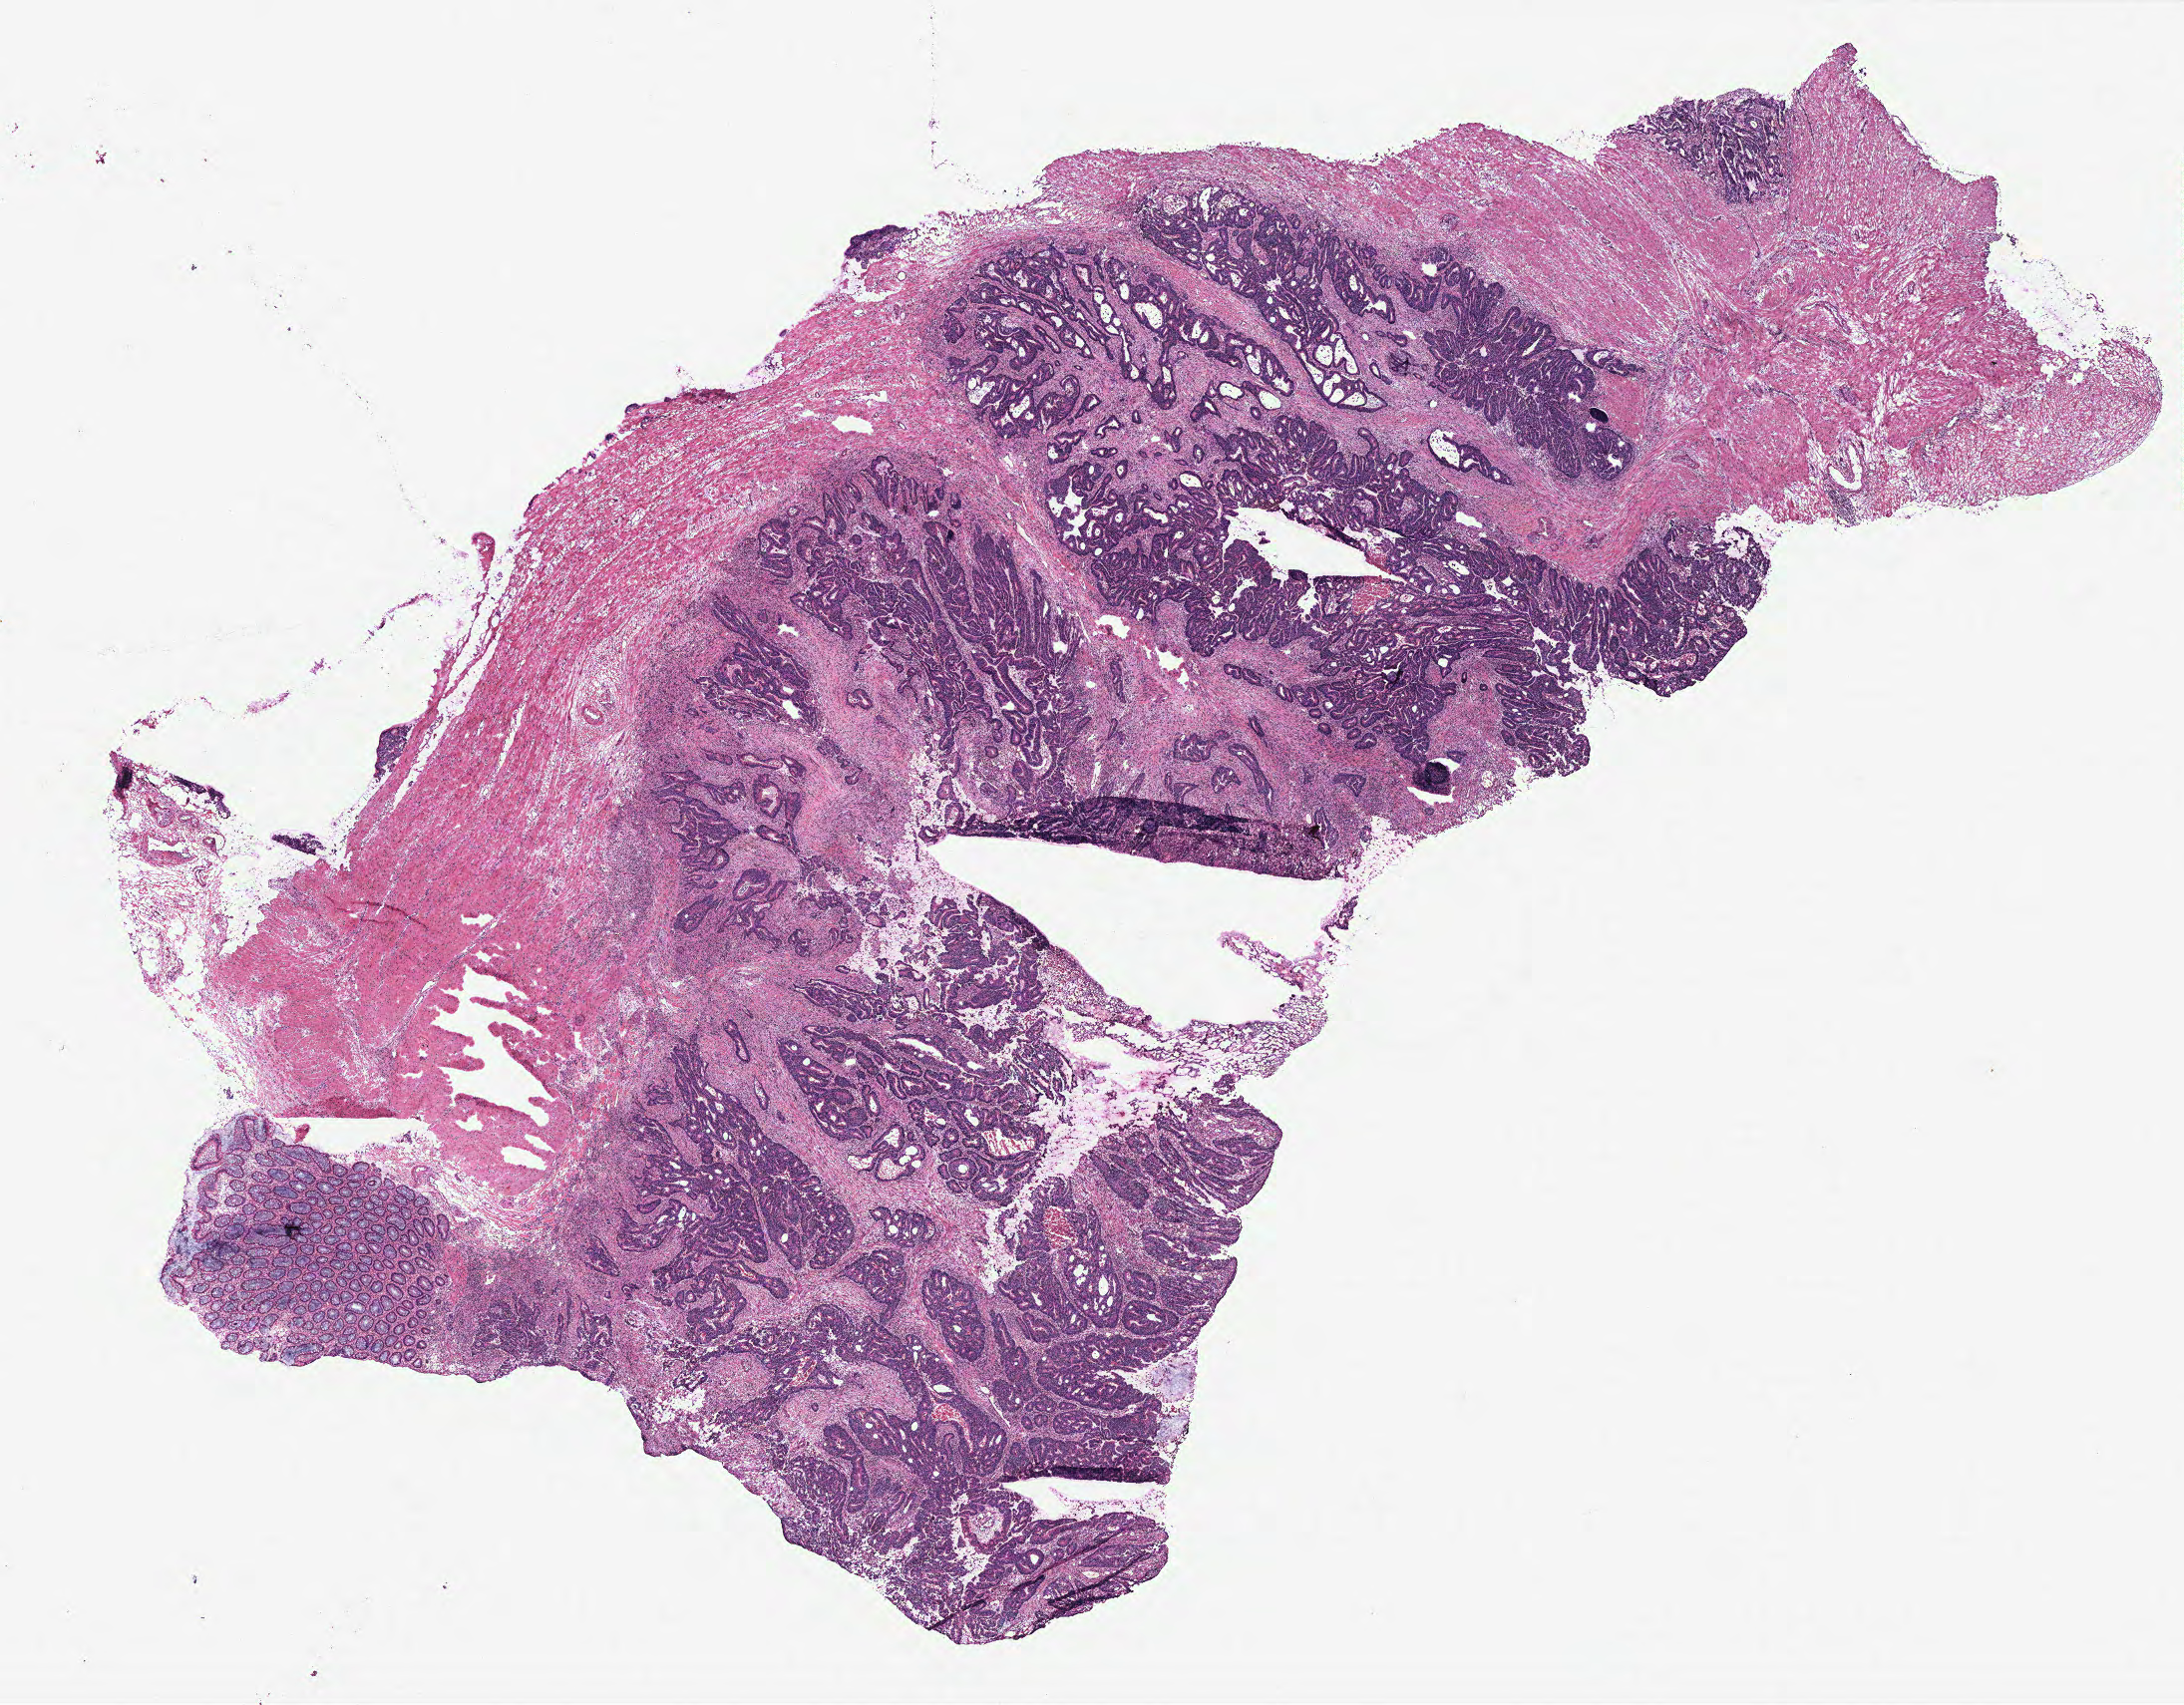
Digitized H&E-stained tissue section (whole slide), low-resolution overview of the scanned area, about 17.5 x 13.7 mm (acquisition: 40x scan). Colon, normal (non-tumour) tissue. Female, 63 y/o.
This section: normal (non-tumour) tissue from the same patient. Patient diagnosis: Adenocarcinoma, NOS.